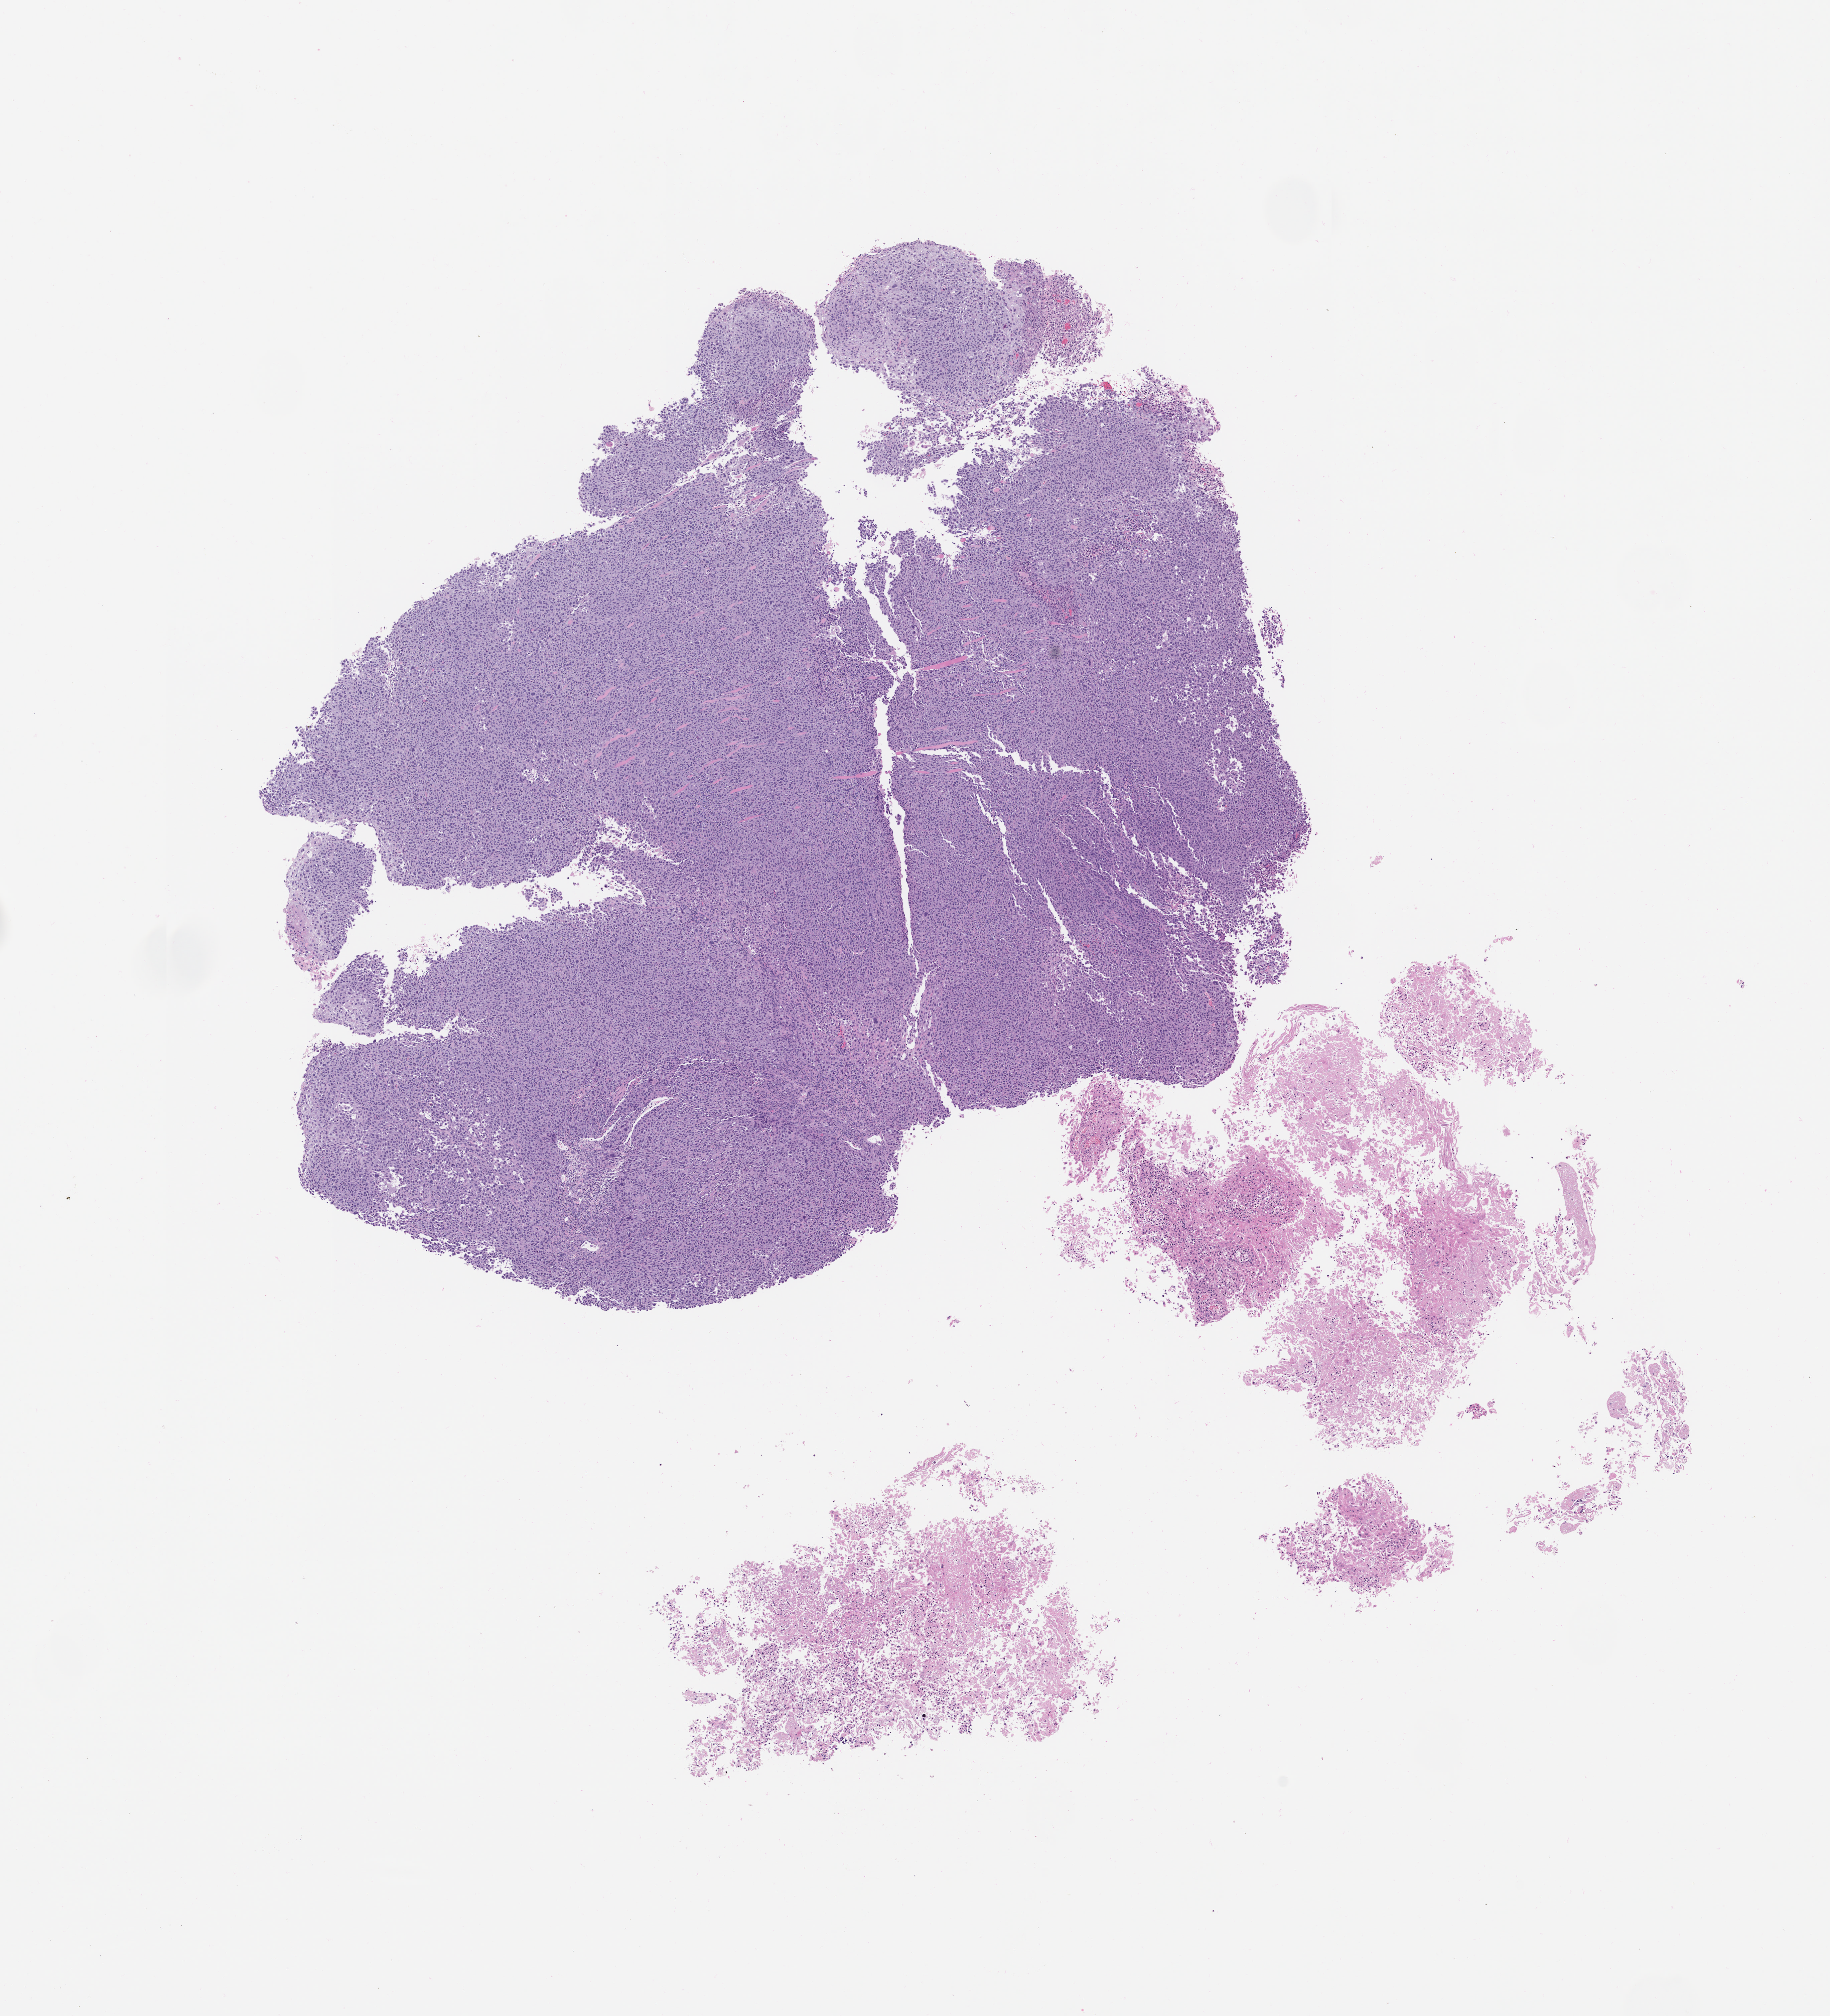
Hematoxylin and eosin (H&E) whole-slide image of a patient-derived xenograft (PDX) tumor grown in a mouse, passage 3, whole scanned area (about 11.0 x 12.1 mm) shown as a low-resolution overview. Formalin-fixed, paraffin-embedded (FFPE) tissue. Originating tumor site category: head and neck.
Originating patient diagnosis: Head and Neck Squamous Cell Carcinoma.